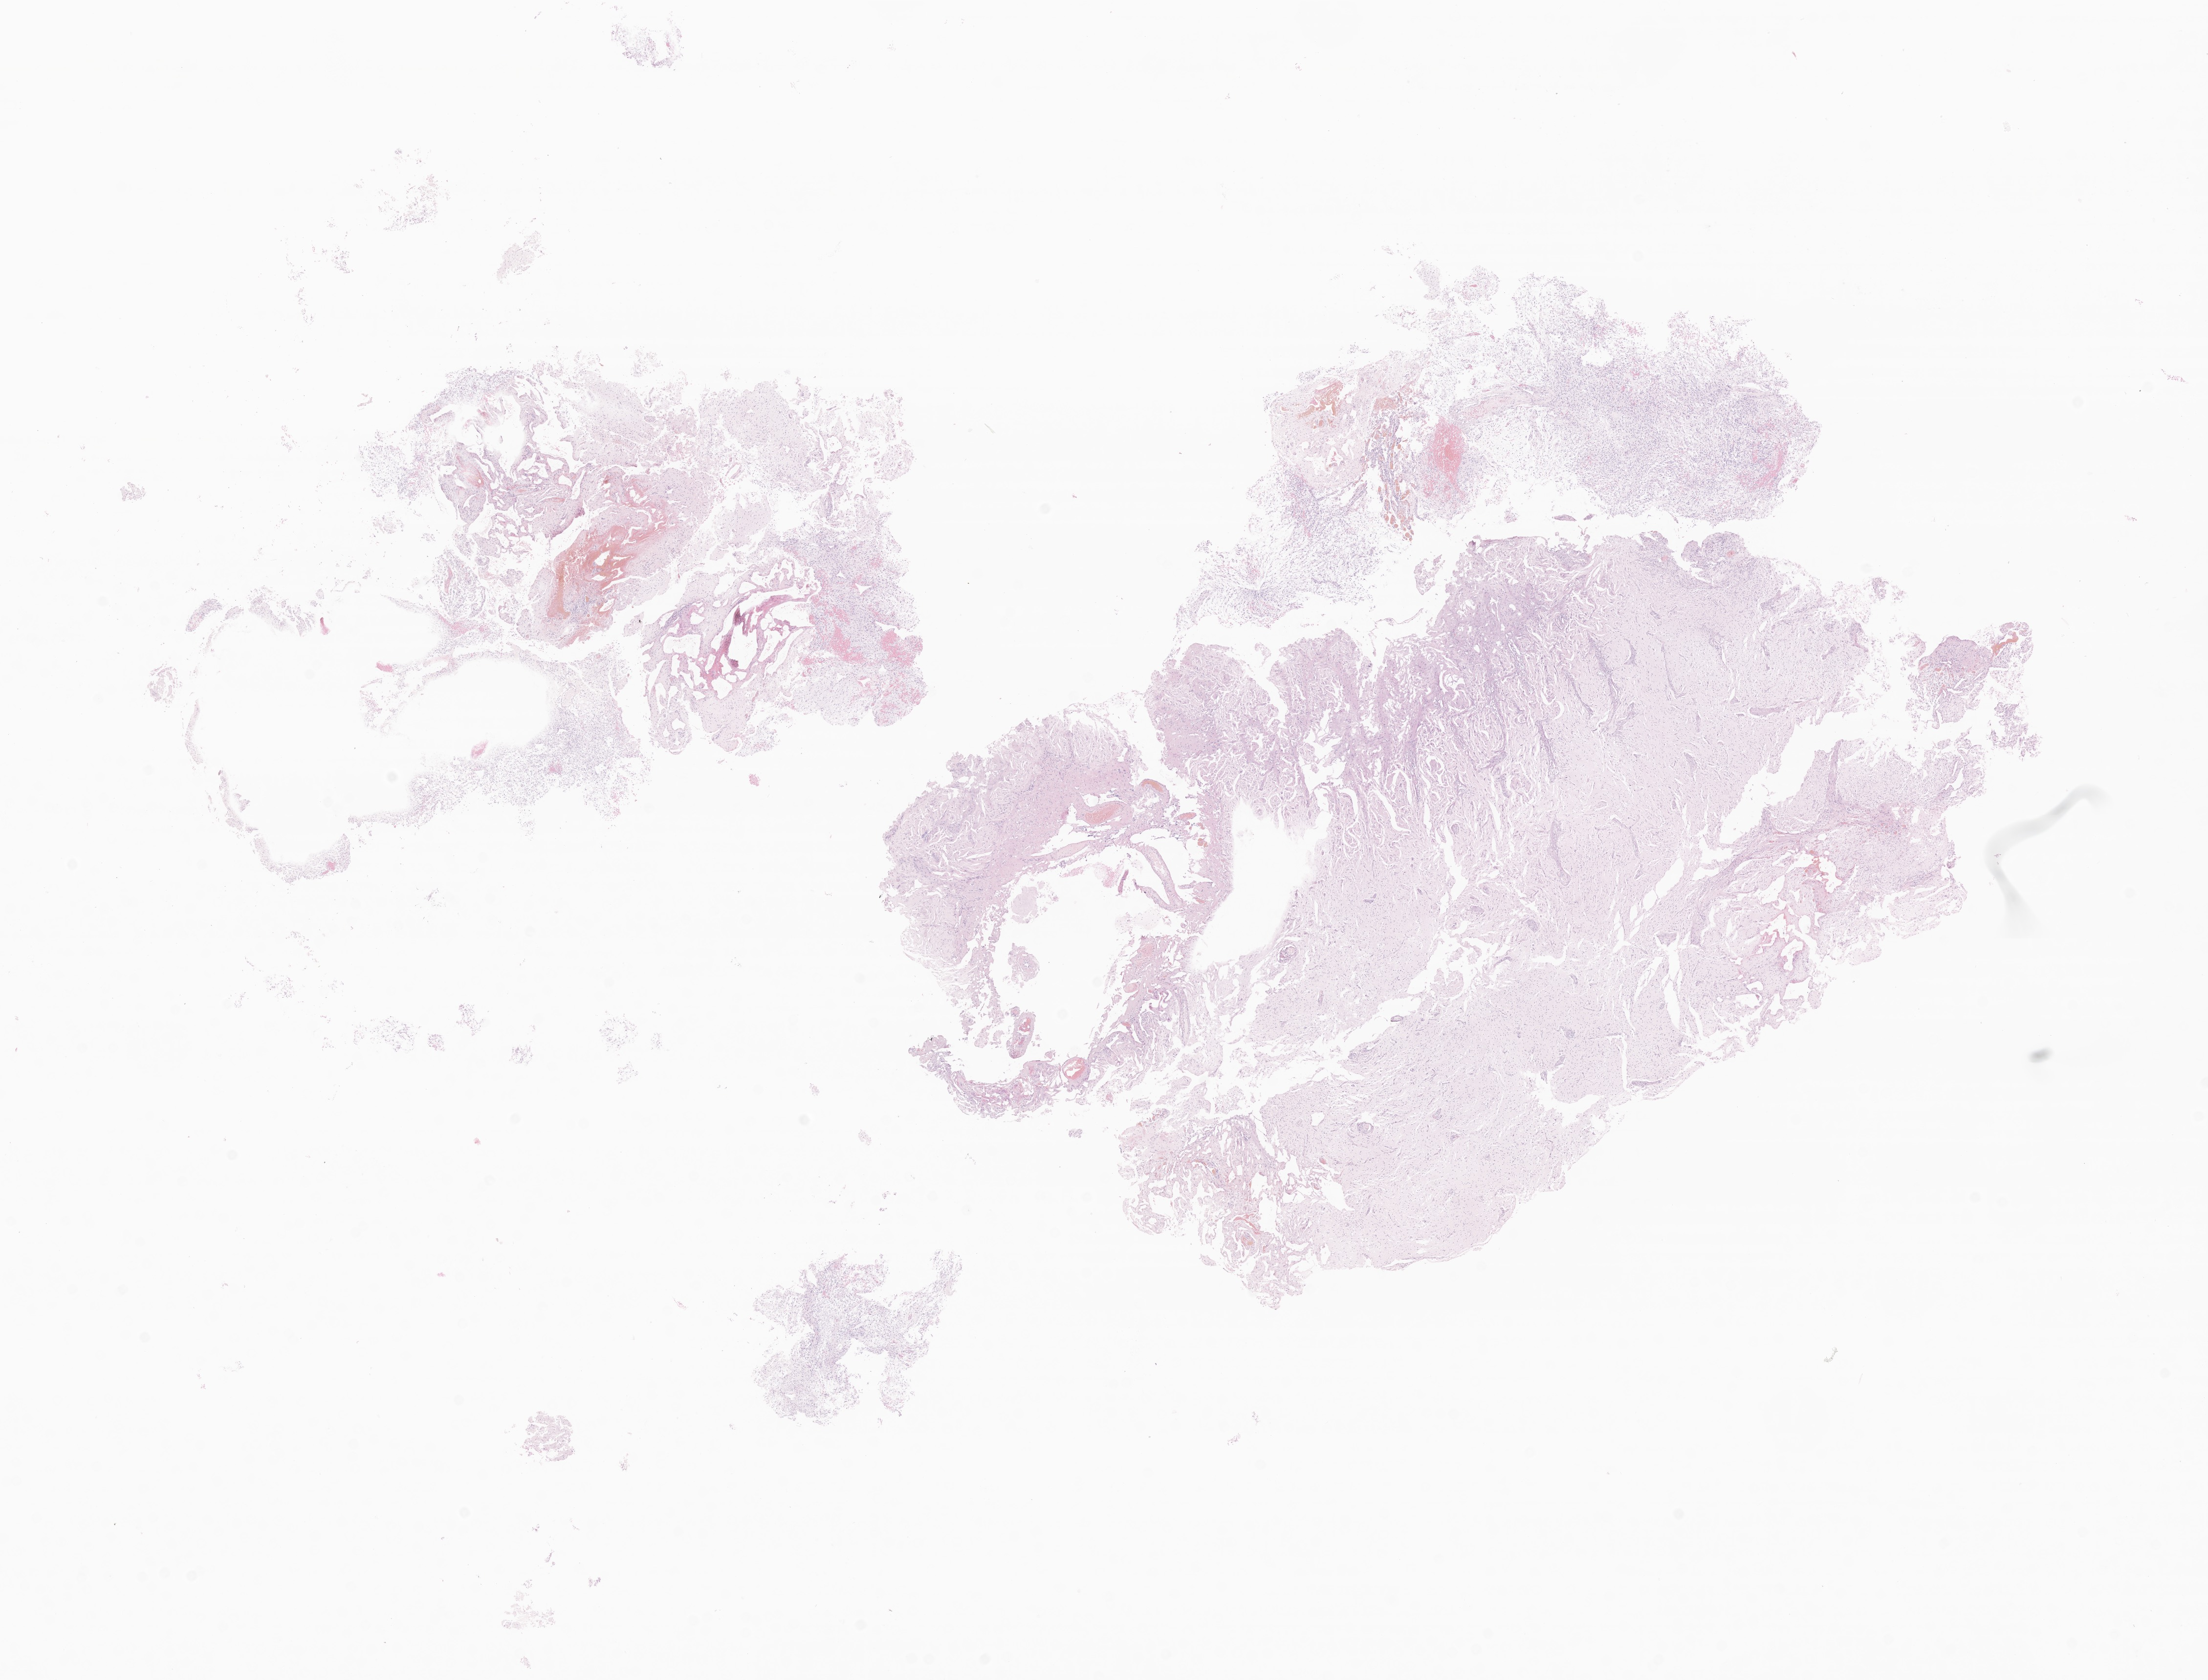
Whole-slide image, haematoxylin and eosin stain of tumor tissue from the brain — low-resolution overview of the scanned area, about 19.0 x 14.5 mm. Formalin-fixed, paraffin-embedded (FFPE) tissue. Male patient, age 59 months (4 years 11 months).
Diagnosis: Pilocytic astrocytoma.